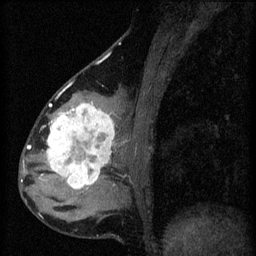
Breast MRI (dynamic contrast-enhanced), one sagittal slice; slice 24 of 60 in the series (ordered by position); 3 images stored at this slice position (order not interpretable as contrast timing); 1.5 T; TE 4.2 ms, TR 8.2 ms; 2 mm slice thickness; 256 × 256 image matrix, field of view 180 × 180 mm. Patient: female, 37 years.
Annotated regions visible in this slice (semi-automatic segmentation, software-assisted and operator-edited):
- analysis volume of interest (the breast-tissue region the enhancement analysis was run in; not a lesion): bounding box <44,100,119,197> (left, top, right, bottom; pixels)
- tumour enhancement mask (voxels above the 70 % enhancement threshold inside the analysis volume of interest): <47,102,116,189>